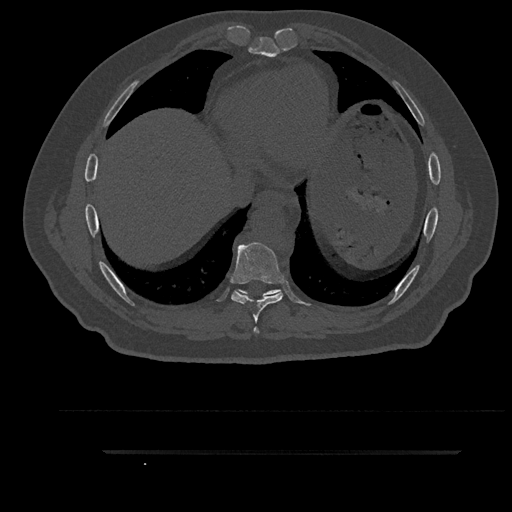
CT including the spine, one axial slice; position 464 of 797 along the scan axis; reconstruction kernel Br40s/3; 120 kVp; bone window (W 1800 / L 400 HU); 512 × 512 image matrix. Male patient, age 63 years. Case-level facts recorded for this patient, not image findings: primary cancer: renal; vertebrae with lytic lesions (as recorded): T8.
Annotated regions visible in this slice (semi-automatically segmented with operator editing):
- T7 vertebra: bounding box (x1, y1, x2, y2) in pixels: (254, 327, 259, 333)
- T8 vertebra: (231, 242, 284, 323)
- T9 vertebra: (236, 289, 281, 297)